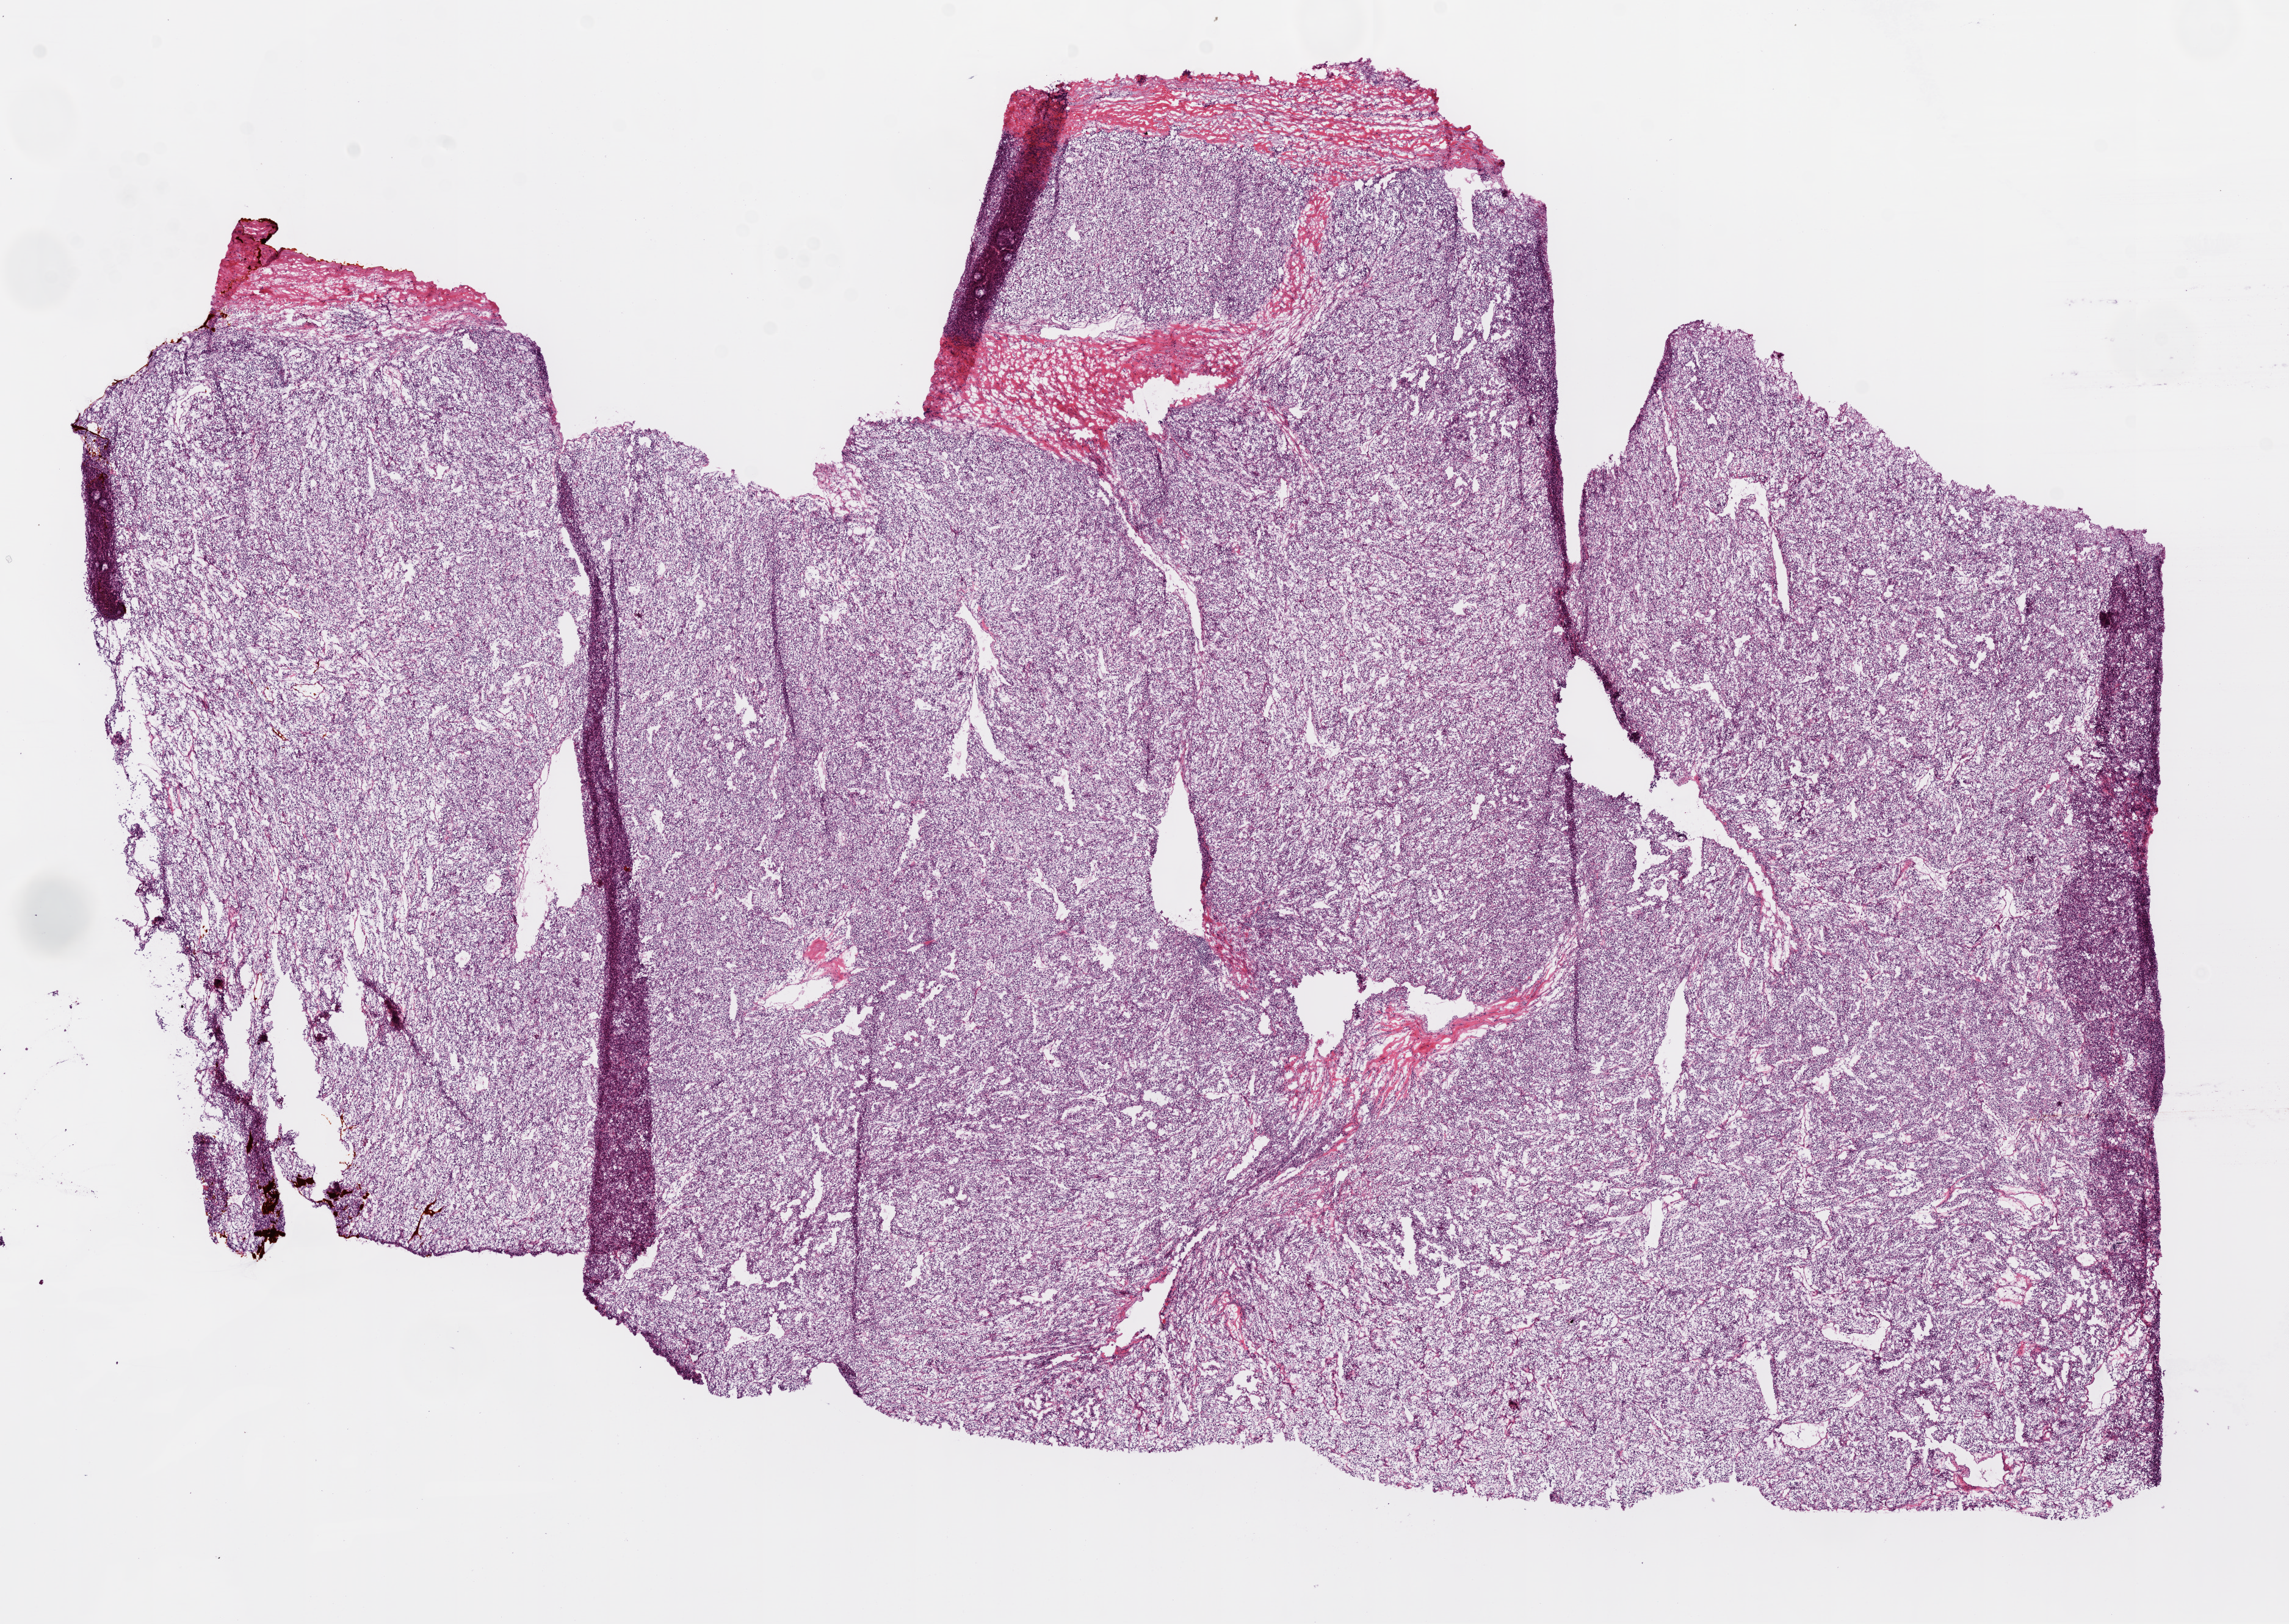
Digitized H&E-stained tissue section (whole slide) — shown as a low-resolution overview of the whole scanned area (about 15.0 x 10.7 mm); frozen section; primary tumour sample from the kidney. Male, age 42 years at initial diagnosis.
Histologic diagnosis: Clear cell adenocarcinoma, NOS.